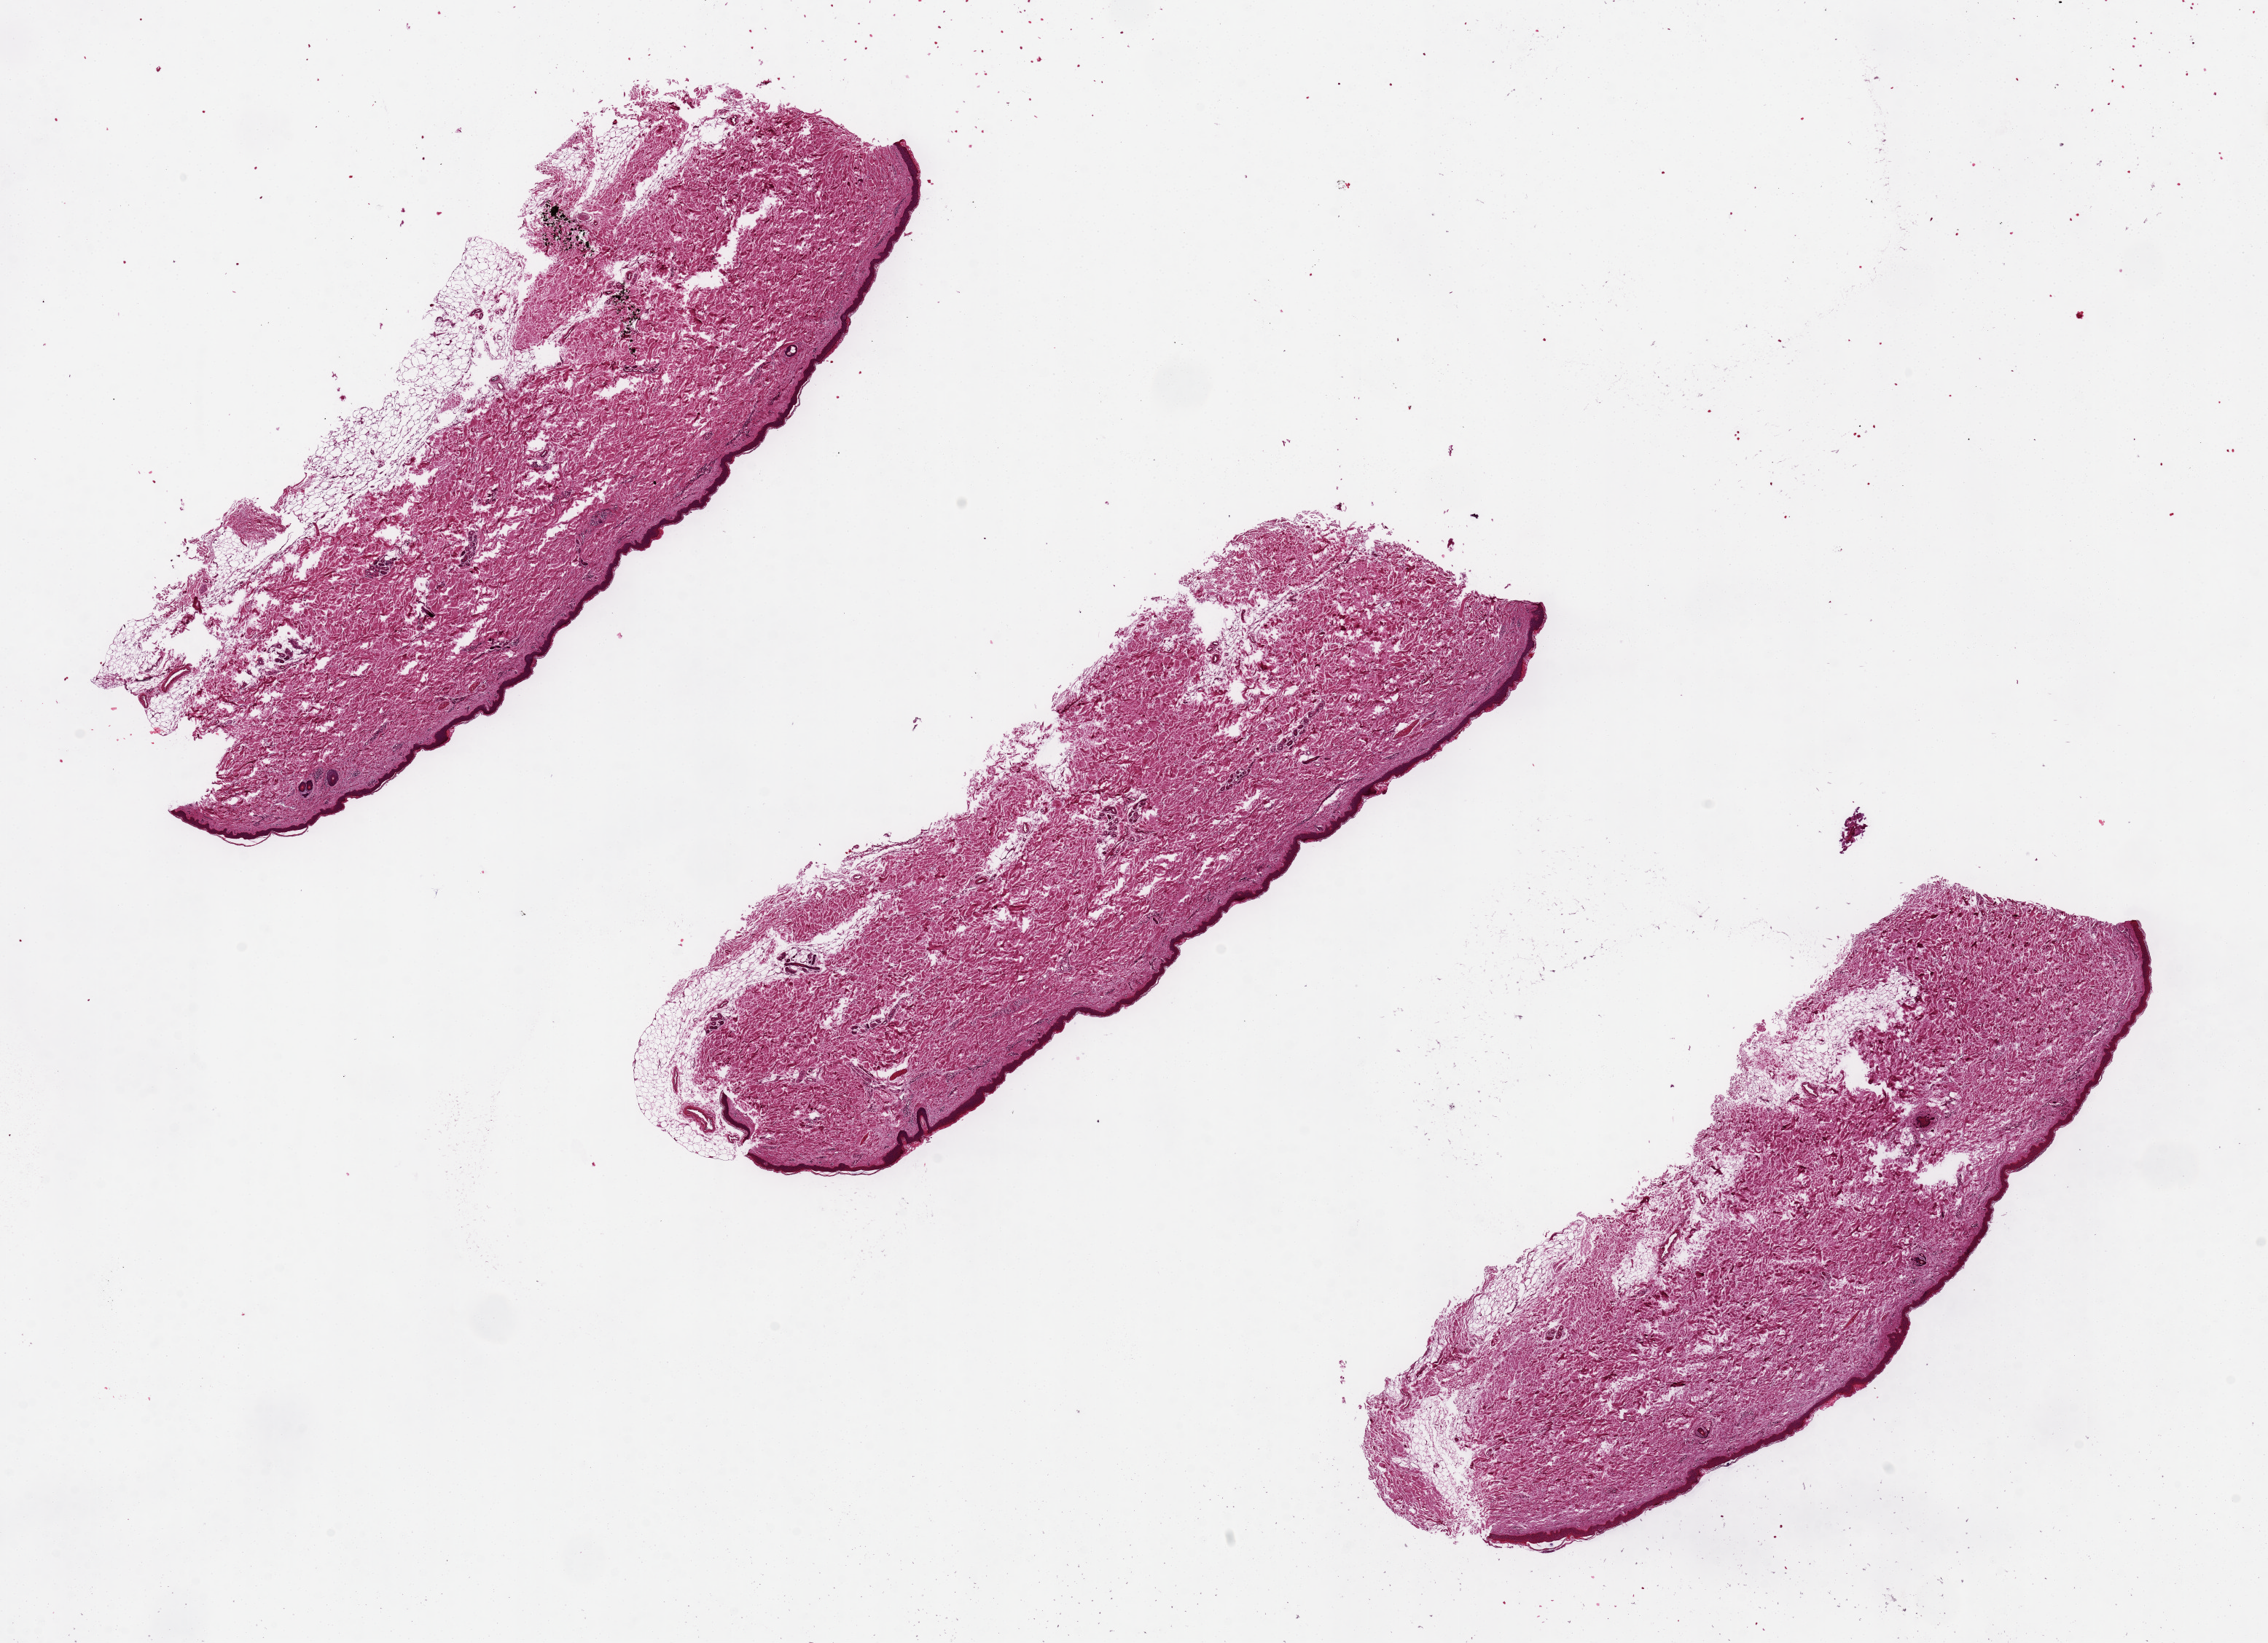
Haematoxylin and eosin whole-slide image, brightfield — a low-resolution overview of the entire scanned area, about 24.6 x 17.8 mm; PAXgene-fixed, paraffin-embedded tissue; target tissue: skin of lower leg; tissue donor sample.
Reviewer comment on this tissue sample: 0-1. 9.7x3mm. Epithelium is ~115micronc, 3-5% of specimen thickness.